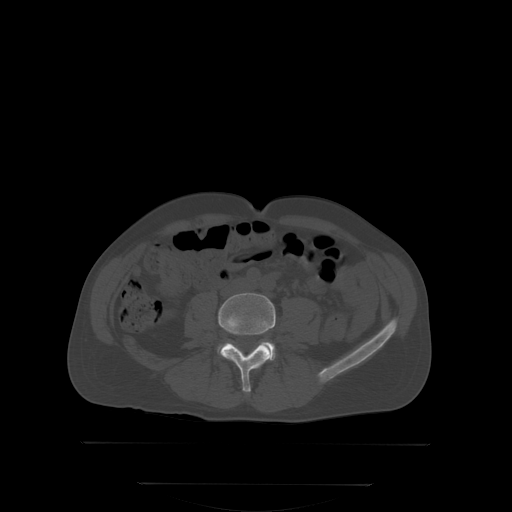
CT including the spine, one axial slice; slice 105 of 350 in the series (ordered by position); bone window (W 1800 / L 400 HU); 2.5 mm slice thickness; 512 × 512 image matrix. Patient: male, 58 years. From the clinical record (not read from this slice): primary cancer: prostate; vertebrae with lytic lesions (as recorded): L1.
Structures marked on this image (semi-automatically segmented with operator editing):
- L4 vertebra: box from (x=218, y=293) to (x=276, y=392) px
- L5 vertebra: (x=225, y=340)–(x=276, y=359)